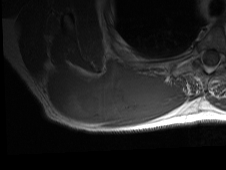
MRI of an extremity soft-tissue mass, one axial slice. Position 28 of 81 along the scan axis. MR volume resampled by the dataset authors to the PET/CT grid (not the native acquisition matrix). 3.27 mm slice thickness. 226 × 170 image matrix, field of view 221 × 166 mm. Male patient. Case-level facts recorded for this patient, not image findings: histological type: pleiomorphic spindle cell undifferentiated; grade: high; site of the primary tumour: right parascapusular.
Annotated regions visible in this slice (expert contour drawn on MRI and transferred to this co-registered scan by the dataset authors):
- gross tumour volume including surrounding oedema: bounding box <46,58,186,126> (left, top, right, bottom; pixels)
- gross tumour volume (mass): <46,59,166,123>